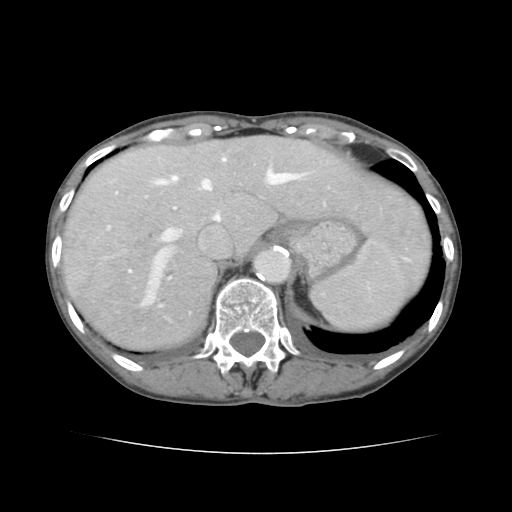
Contrast-enhanced abdominal CT, one axial slice; position 109 of 136 along the scan axis; 120 kVp; intravenous contrast given; soft-tissue window (W 400 / L 40 HU); 2.5 mm slice thickness; 512 × 512 image matrix. Female patient, age 77 years. From the clinical record (not read from this slice): diagnosis: colorectal cancer liver metastases, imaged before liver resection; multiple liver metastases: yes; largest metastasis: 3 cm; disease in both lobes: no.
Structures marked on this image (outlined manually by an expert reader):
- hepatic veins: bounding box <105,158,303,304> (left, top, right, bottom; pixels)
- liver: <61,136,430,350>
- planned liver remnant (the part of the liver to remain after resection): <165,136,430,278>
- portal vein (with intrahepatic branches): <108,185,382,279>